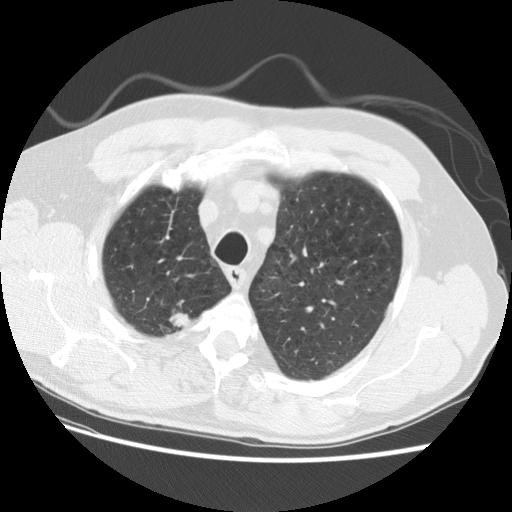
Low-dose screening chest CT, axial slice. Baseline screening round. Lung window (W 1500 / L -600 HU). Slice 23 of 124 in the series. 512 × 512 image matrix, field of view 361 × 361 mm. Male participant, aged 69 years at enrolment.
- Lesion marked by an expert reader, bounding box (x1, y1, x2, y2) in pixels: (159, 304, 201, 336).
- Screening reader's record for this exam (one nodule recorded; not confirmed to be the boxed lesion): non-calcified nodule or mass ≥4 mm, right upper lobe, 15 × 15 mm, spiculated (stellate) margins, soft tissue attenuation.
- Later outcome: lung cancer diagnosed 22 days after this screen — large cell neuroendocrine carcinoma, right upper lobe, poorly differentiated (G3), stage IA (AJCC 6th edition), 23 mm at pathology.